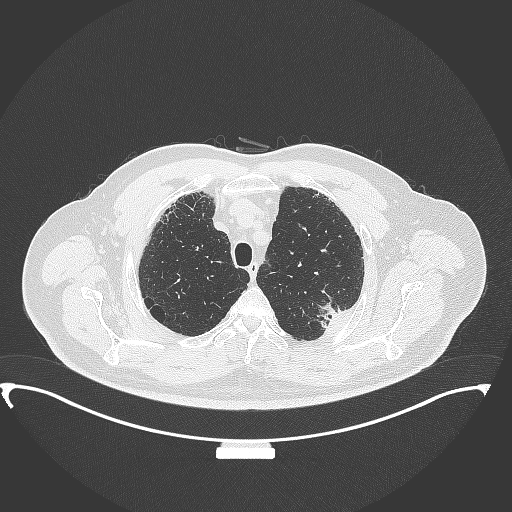
Chest CT, one axial slice; position 297 of 350 along the scan axis; reconstruction kernel B70f; lung window (W 1500 / L -600 HU); 1 mm slice thickness; 512 × 512 image matrix. Patient: male, 64 years. From the clinical record (not read from this slice): clinical TNM (as recorded): T1c N1 M1.
Outlined on this slice (rectangle marked by the reading radiologist):
- lung tumour (recorded histology: adenocarcinoma): bounding box [x1, y1, x2, y2] px = [315, 301, 353, 334]